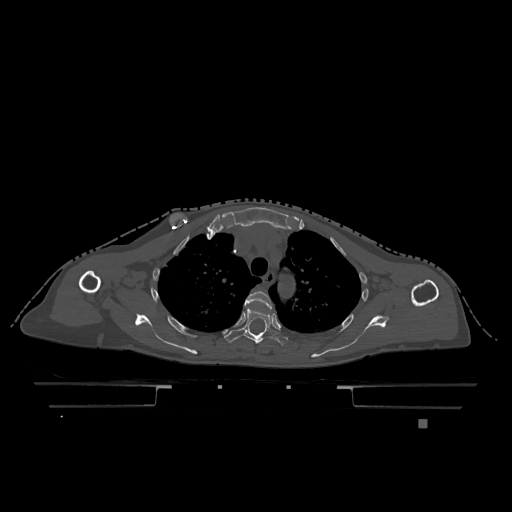
CT including the spine, one axial slice; position 892 of 1317 along the scan axis; bone window (W 1800 / L 400 HU); 512 × 512 image matrix, field of view 500 × 500 mm. Female patient, age 74 years. Case-level facts recorded for this patient, not image findings: primary cancer: lung.
Outlined on this slice (semi-automatically segmented with operator editing):
- T3 vertebra: box from (x=245, y=291) to (x=272, y=308) px
- T4 vertebra: (x=224, y=307)–(x=288, y=347)